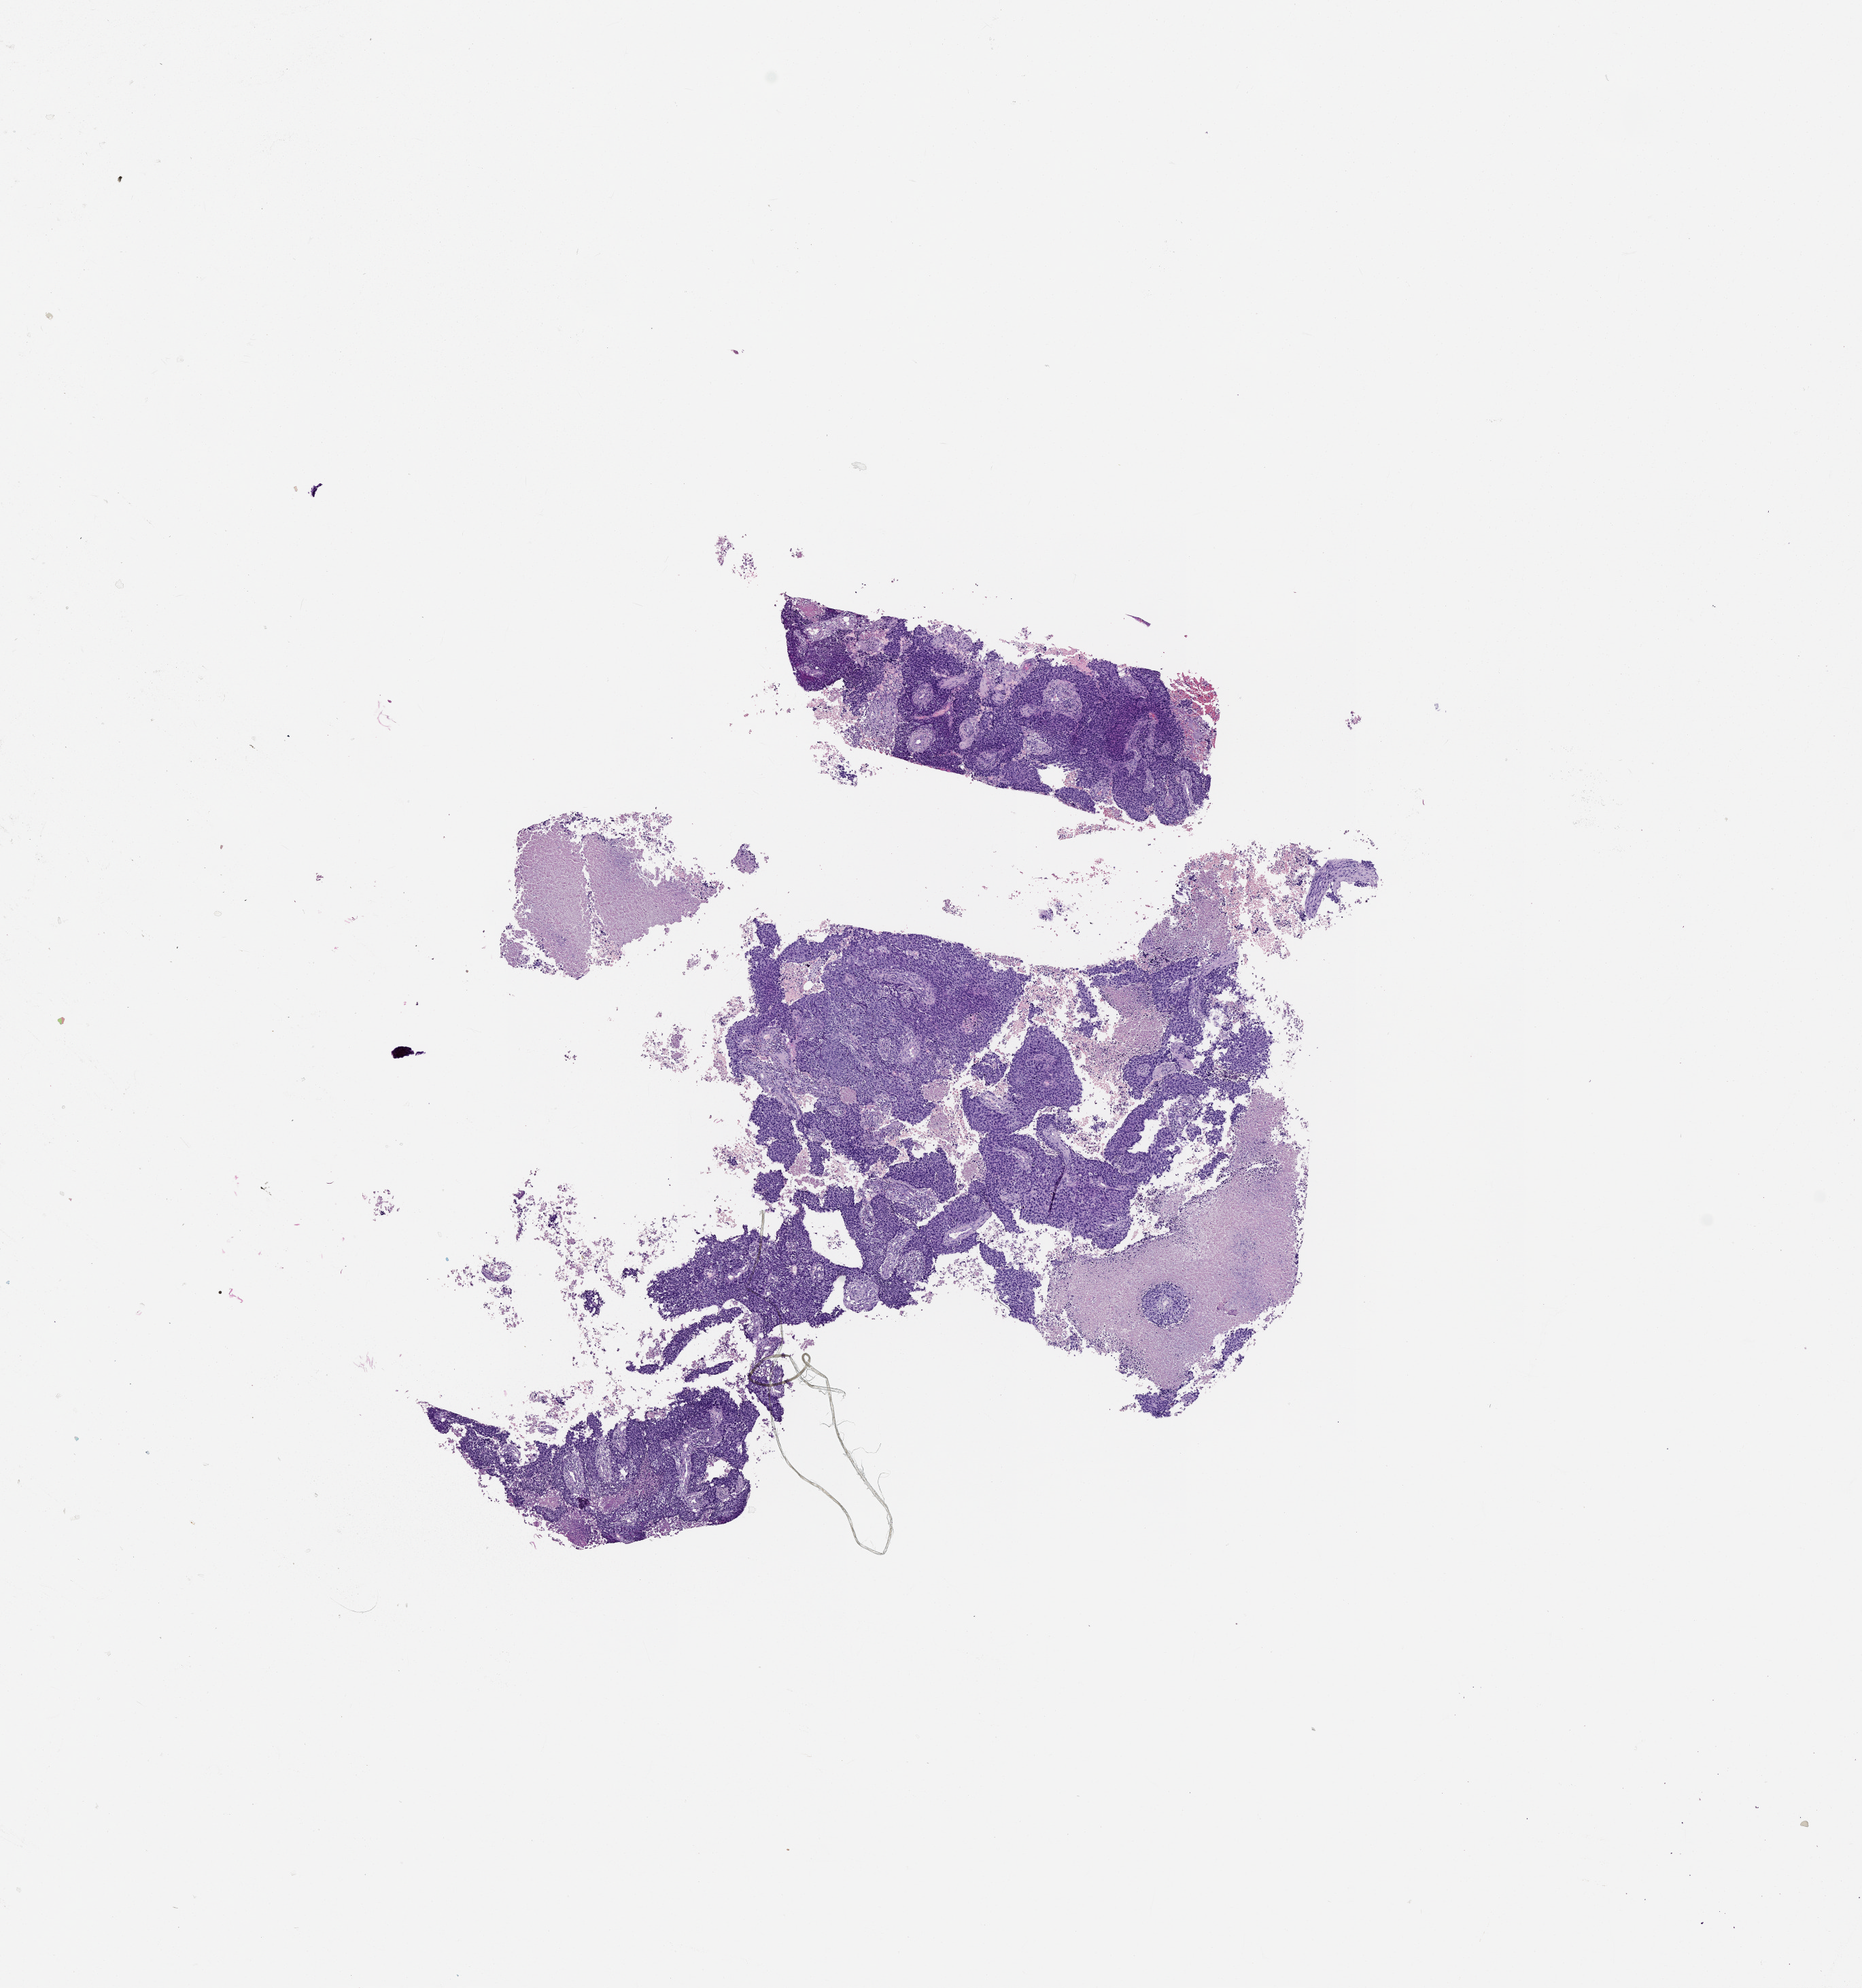
H&E-stained whole-slide image, a low-resolution overview of the entire scanned area, about 11.0 x 11.8 mm (slide scanned at 20x), lung, tumour tissue. Male, 60 y/o.
Patient diagnosis (cohort enrolment): squamous cell carcinoma (lung).